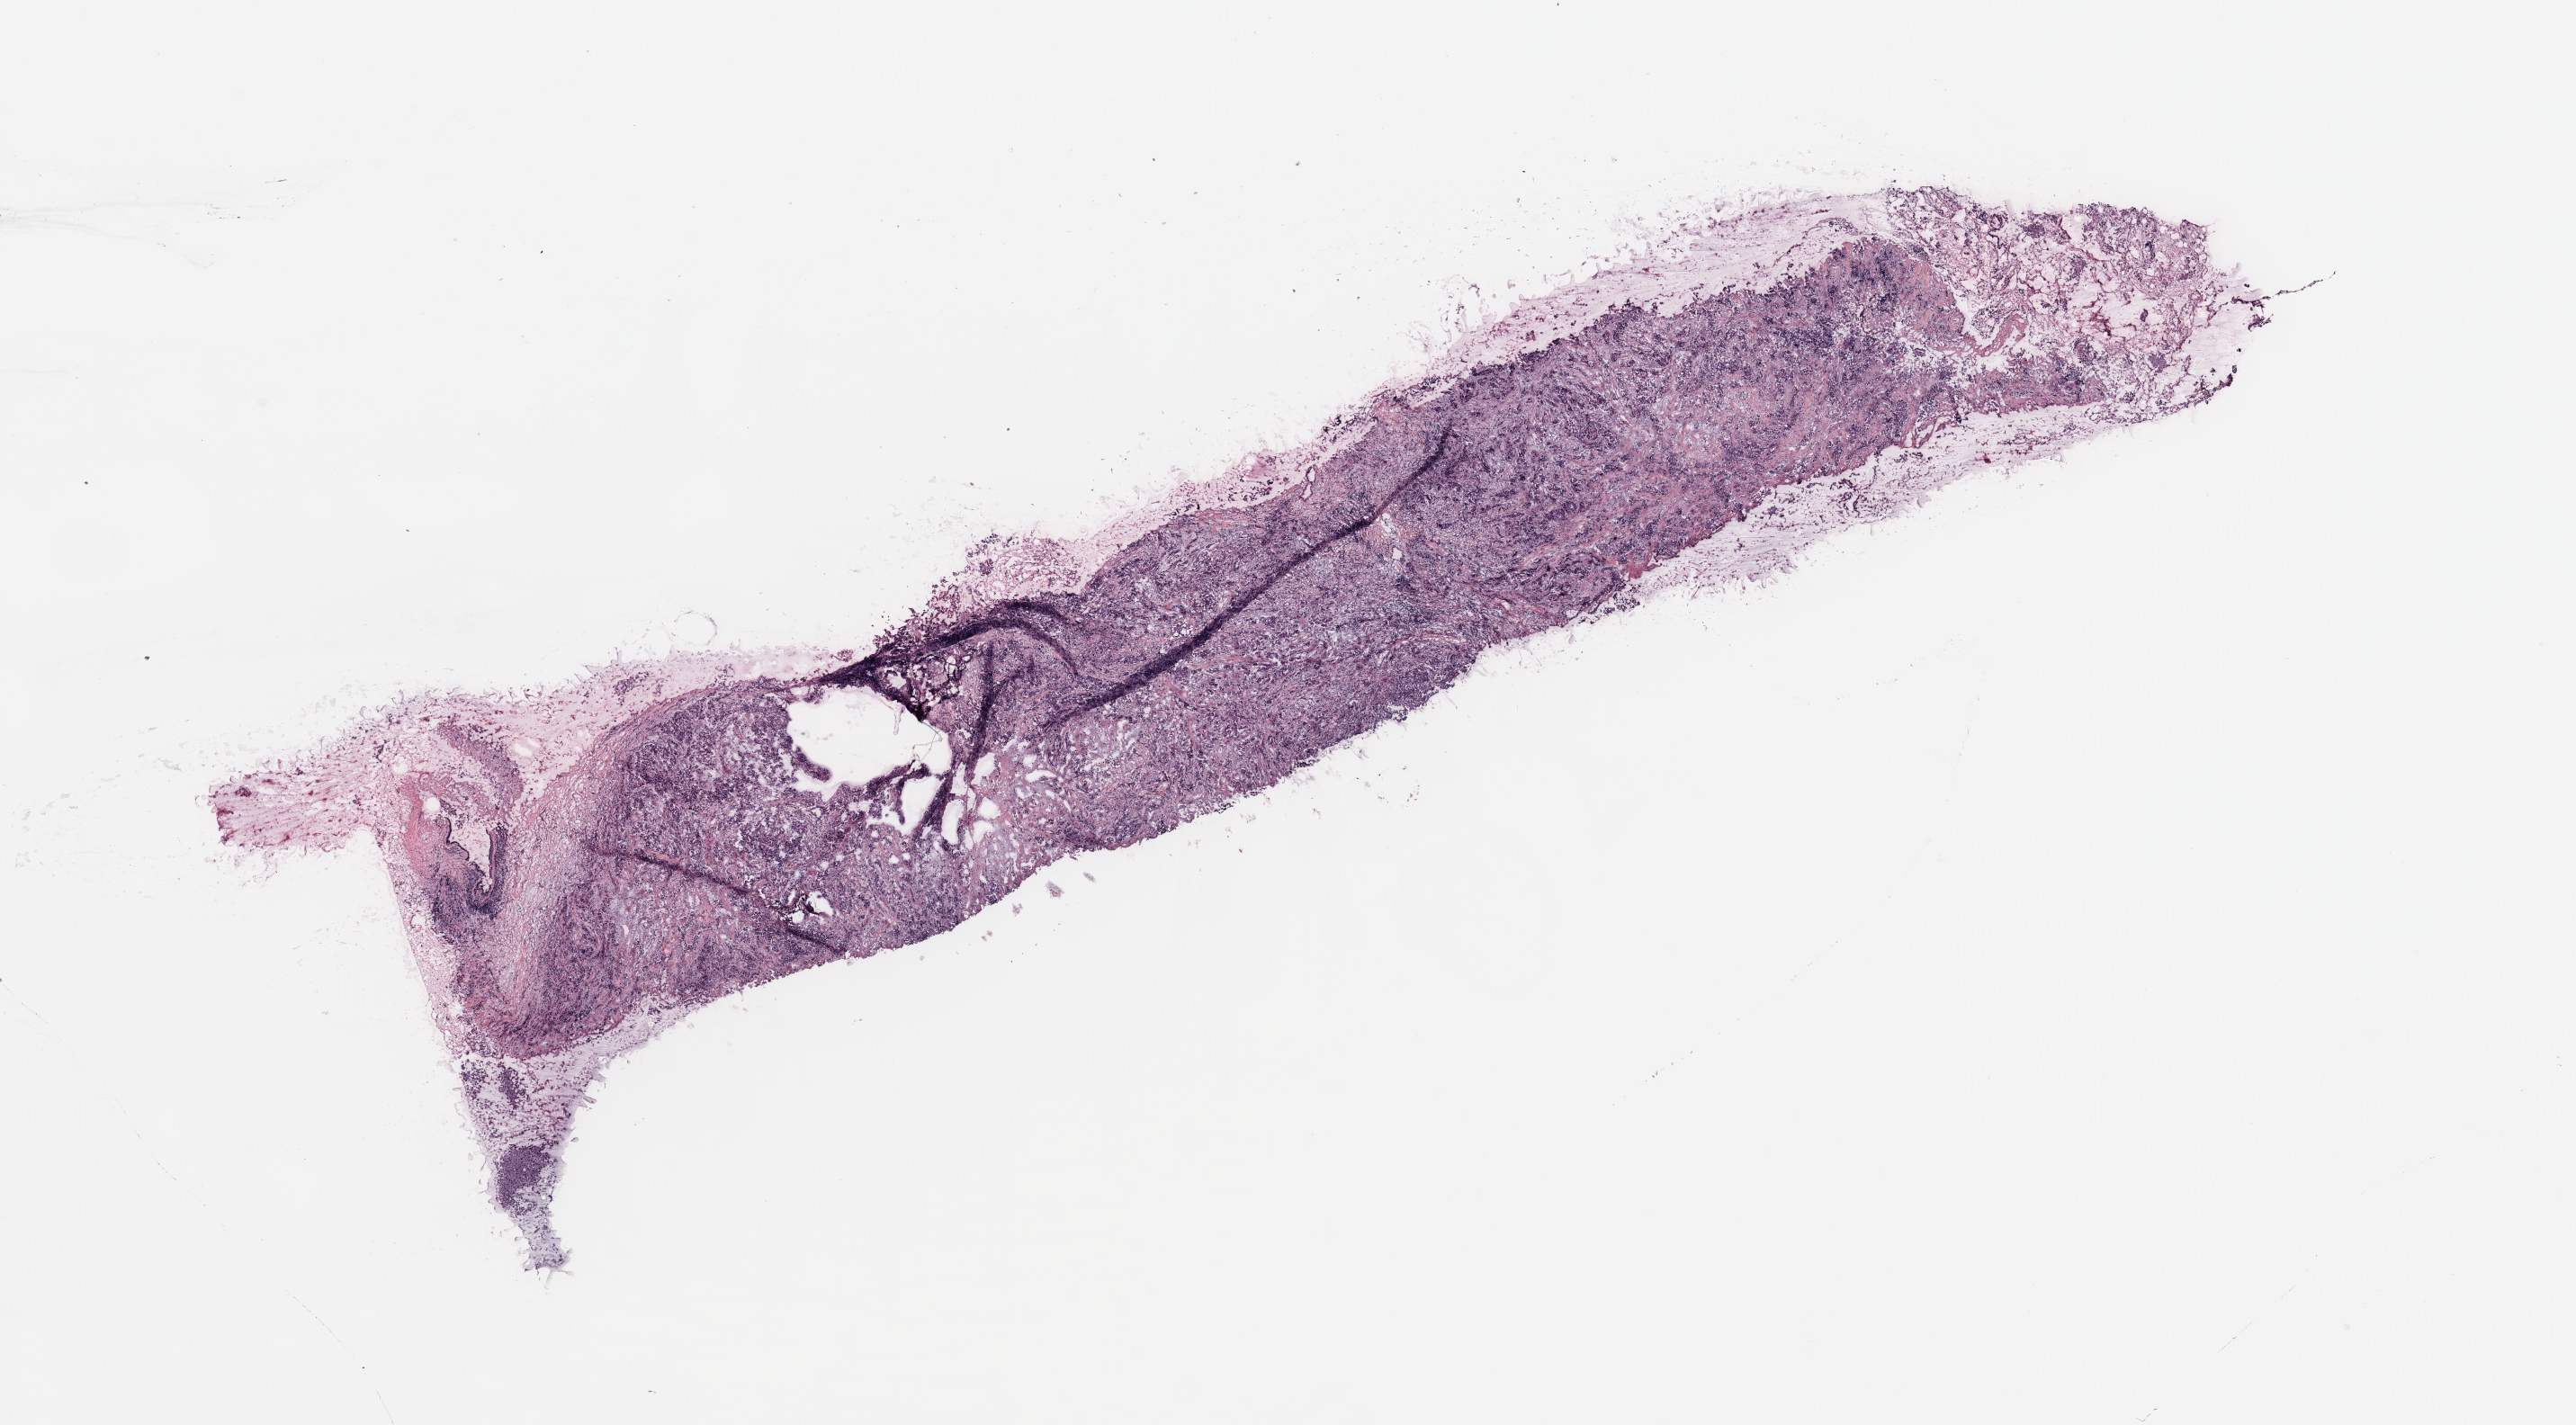
H&E-stained whole-slide image, shown as a low-resolution overview of the whole scanned area (about 22.6 x 12.5 mm, slide scanned at 20x); breast, tissue type not recorded.
Patient diagnosis (cohort enrolment): breast cancer (breast).